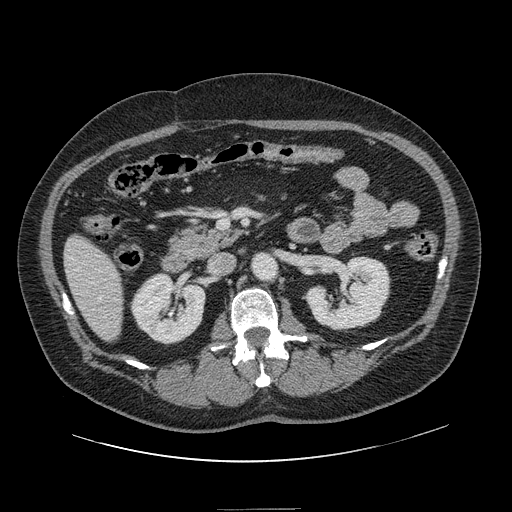
Contrast-enhanced abdominal CT, one axial slice; position 50 of 154 along the scan axis; soft-tissue window (W 400 / L 40 HU); 512 × 512 image matrix, field of view 451 × 451 mm. Male patient, age 61 years. From the clinical record (not read from this slice): diagnosis: colorectal cancer liver metastases, imaged before liver resection; multiple liver metastases: yes; largest metastasis: 2.6 cm.
Outlined on this slice (expert manual segmentation):
- hepatic veins: bounding box (x1, y1, x2, y2) in pixels: (75, 267, 102, 301)
- liver: (65, 237, 122, 341)
- planned liver remnant (the part of the liver to remain after resection): (65, 237, 122, 341)